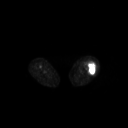
FDG PET of an extremity soft-tissue mass (from a PET/CT study), one axial slice; position 203 of 267 along the scan axis; 3.27 mm slice thickness; 128 × 128 image matrix, field of view 700 × 700 mm. Patient: female, 62 years. Case-level facts recorded for this patient, not image findings: histological type: undifferentiated – high grade; grade: high; site of the primary tumour: left thigh.
Annotated regions visible in this slice (expert contour drawn on MRI and transferred to this co-registered scan by the dataset authors):
- gross tumour volume including surrounding oedema: bounding box <84,61,96,74> (left, top, right, bottom; pixels)
- gross tumour volume (mass): <90,62,95,74>